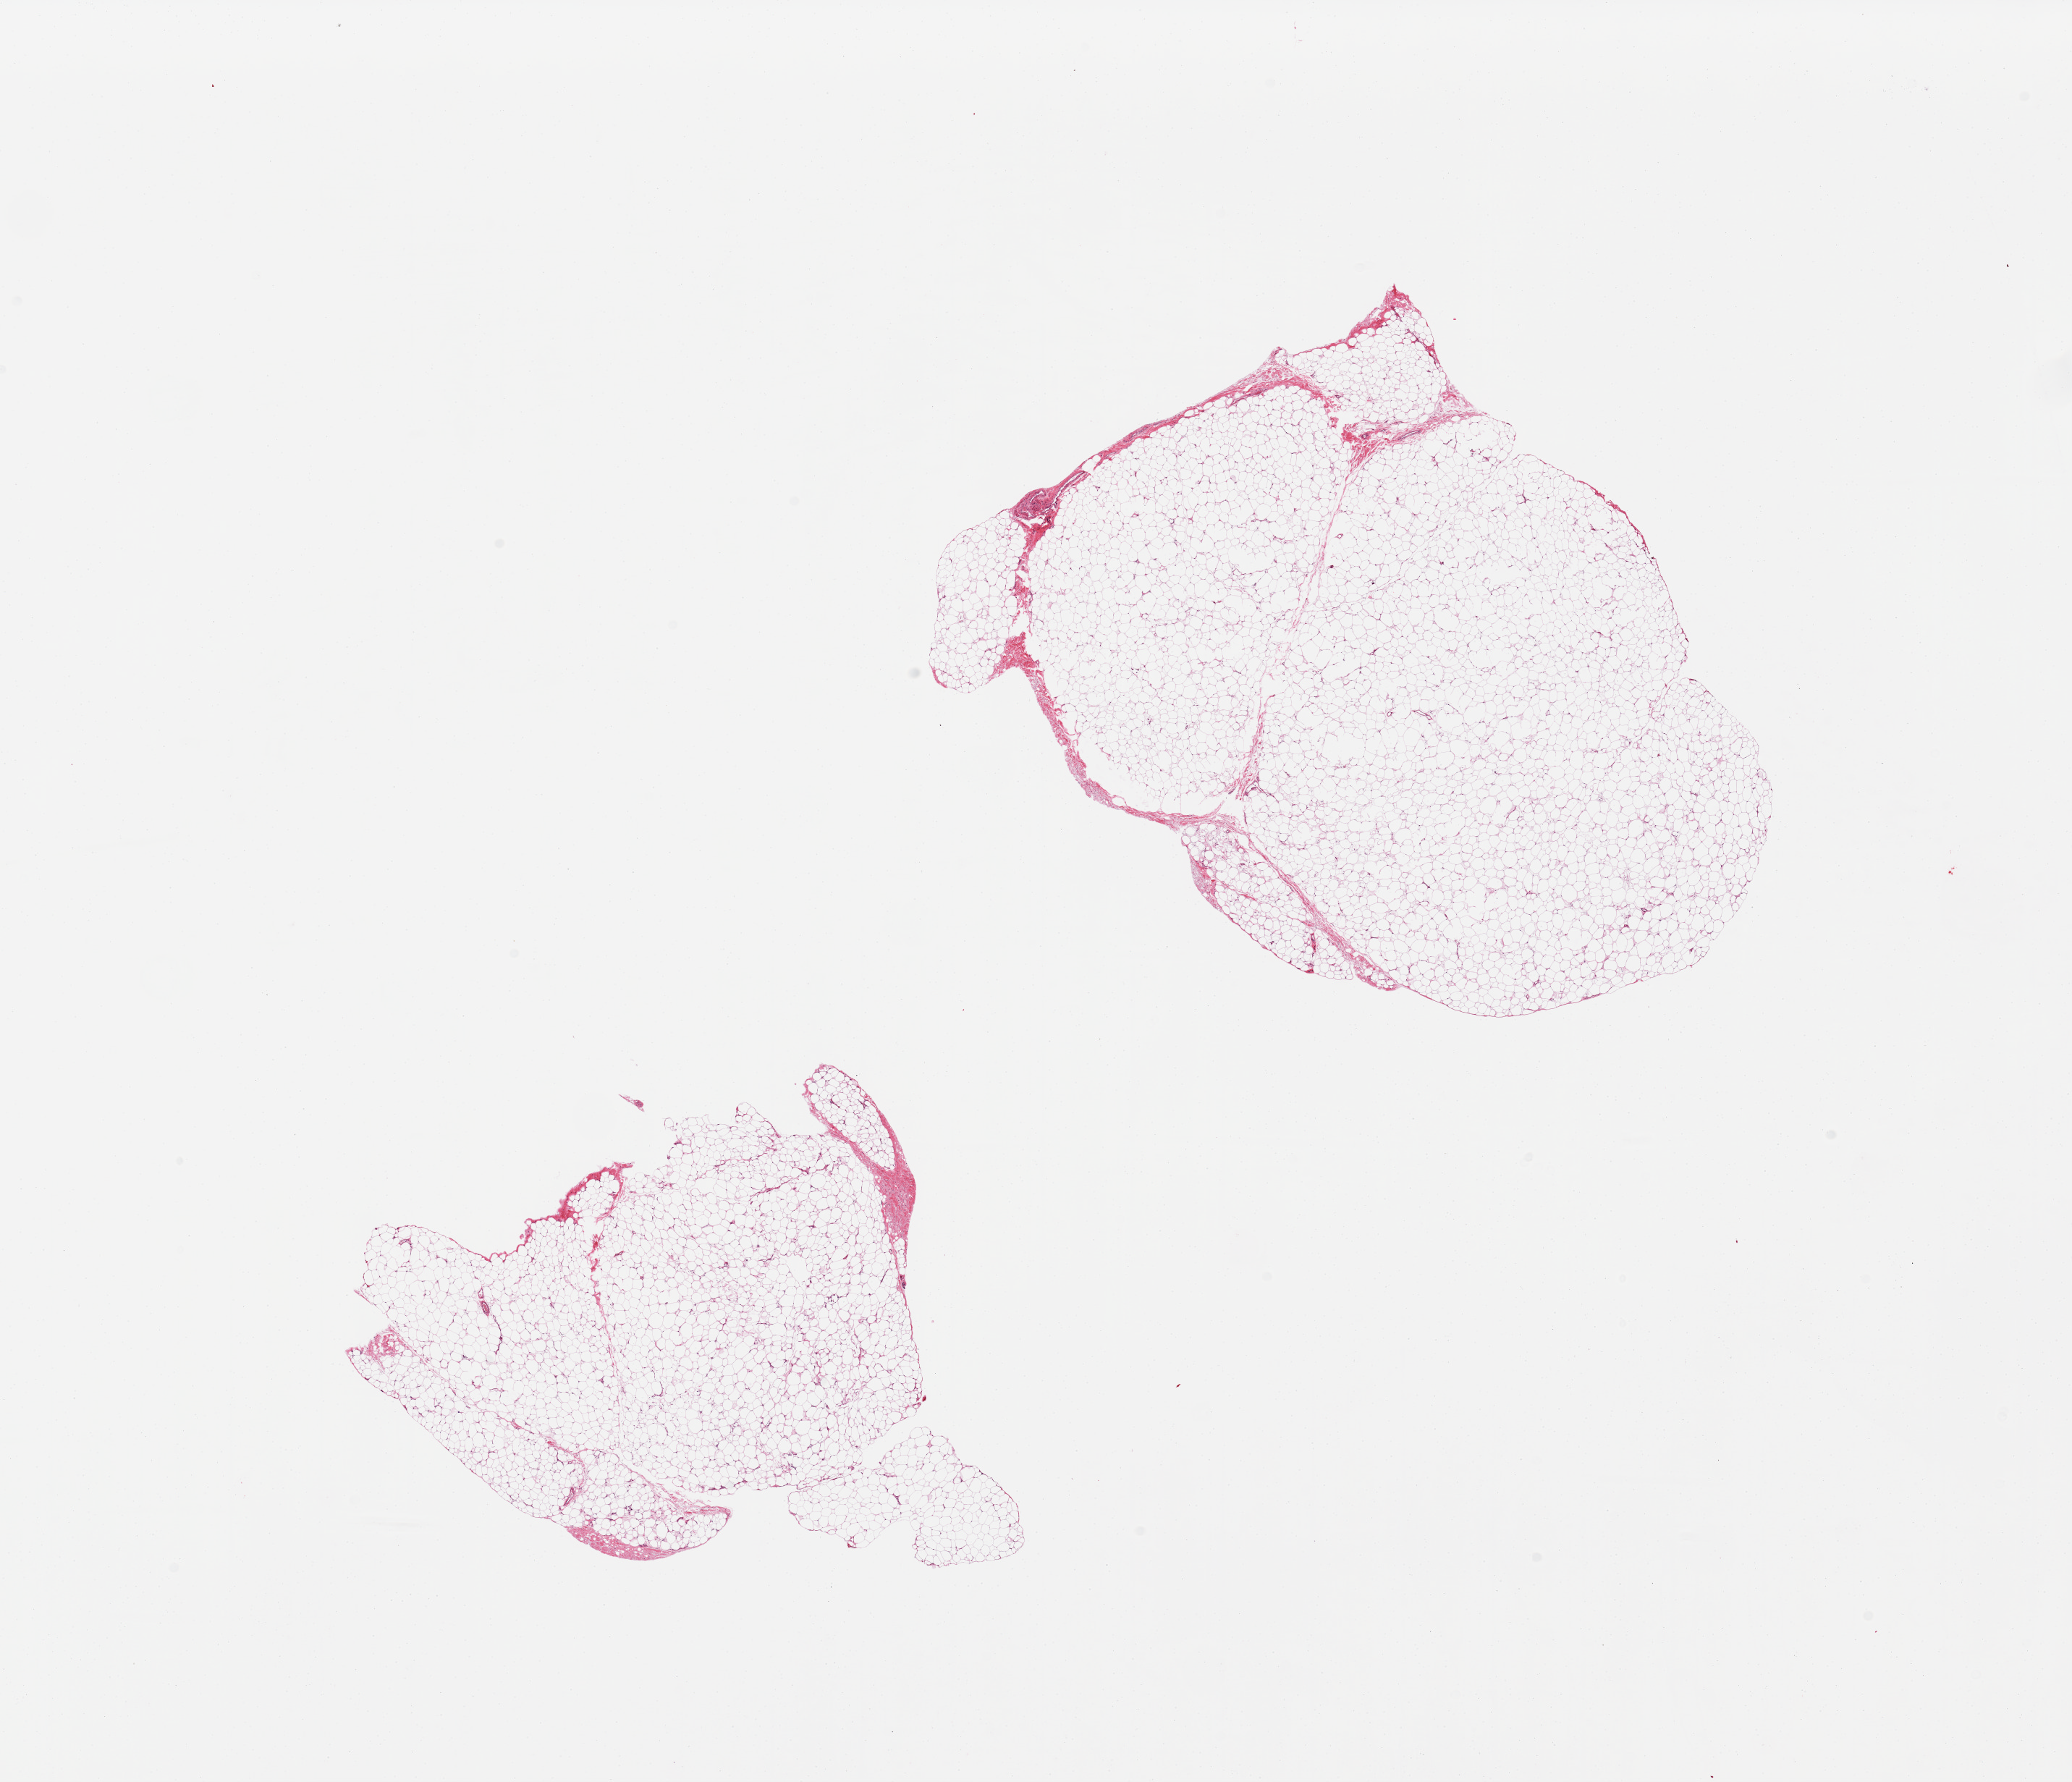
Haematoxylin and eosin whole-slide image — shown as a low-resolution overview of the whole scanned area (about 22.6 x 19.5 mm, acquisition: 20x scan). PAXgene-fixed paraffin-embedded (PFPE) section. Target tissue: adipose tissue. Tissue donor sample. Donor sex: male.
Reviewer comment on this tissue sample: 2 pieces, scant fibrous tissue, good specimens.